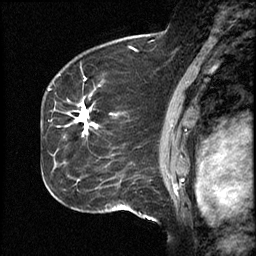
Breast MRI (dynamic contrast-enhanced), one sagittal slice; position 31 of 46 along the scan axis; dynamic contrast-enhanced study with each time point stored as its own series, time point 2 of 4 at this slice position (early post-contrast, ordered by acquisition time); 1.5 T; TE 4.2 ms, TR 18.3 ms; 256 × 256 image matrix, field of view 200 × 200 mm. Case-level facts recorded for this patient, not image findings: setting: breast cancer imaged before/during neoadjuvant chemotherapy; receptor status: HR-positive, HER2-negative.
Annotated regions visible in this slice (semi-automatically segmented with operator editing):
- analysis volume of interest (the breast-tissue region the enhancement analysis was run in; not a lesion): bounding box (x1, y1, x2, y2) in pixels: (64, 71, 111, 209)
- tumour enhancement mask (voxels above the 100 % enhancement threshold inside the analysis volume of interest): (77, 103, 89, 129)